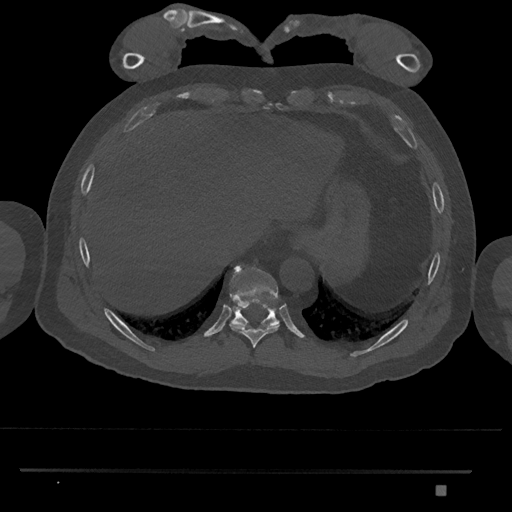
CT including the spine, one axial slice; slice 1032 of 1134 in the series (ordered by position); reconstruction kernel Br40s/3; bone window (W 1800 / L 400 HU); 0.5 mm slice thickness; 512 × 512 image matrix, field of view 429 × 429 mm. Patient: male, 65 years. Case-level facts recorded for this patient, not image findings: primary cancer: prostate.
Annotated regions visible in this slice (semi-automatic segmentation, software-assisted and operator-edited):
- T10 vertebra: bounding box [x1, y1, x2, y2] px = [229, 265, 279, 328]
- T9 vertebra: [229, 322, 280, 348]